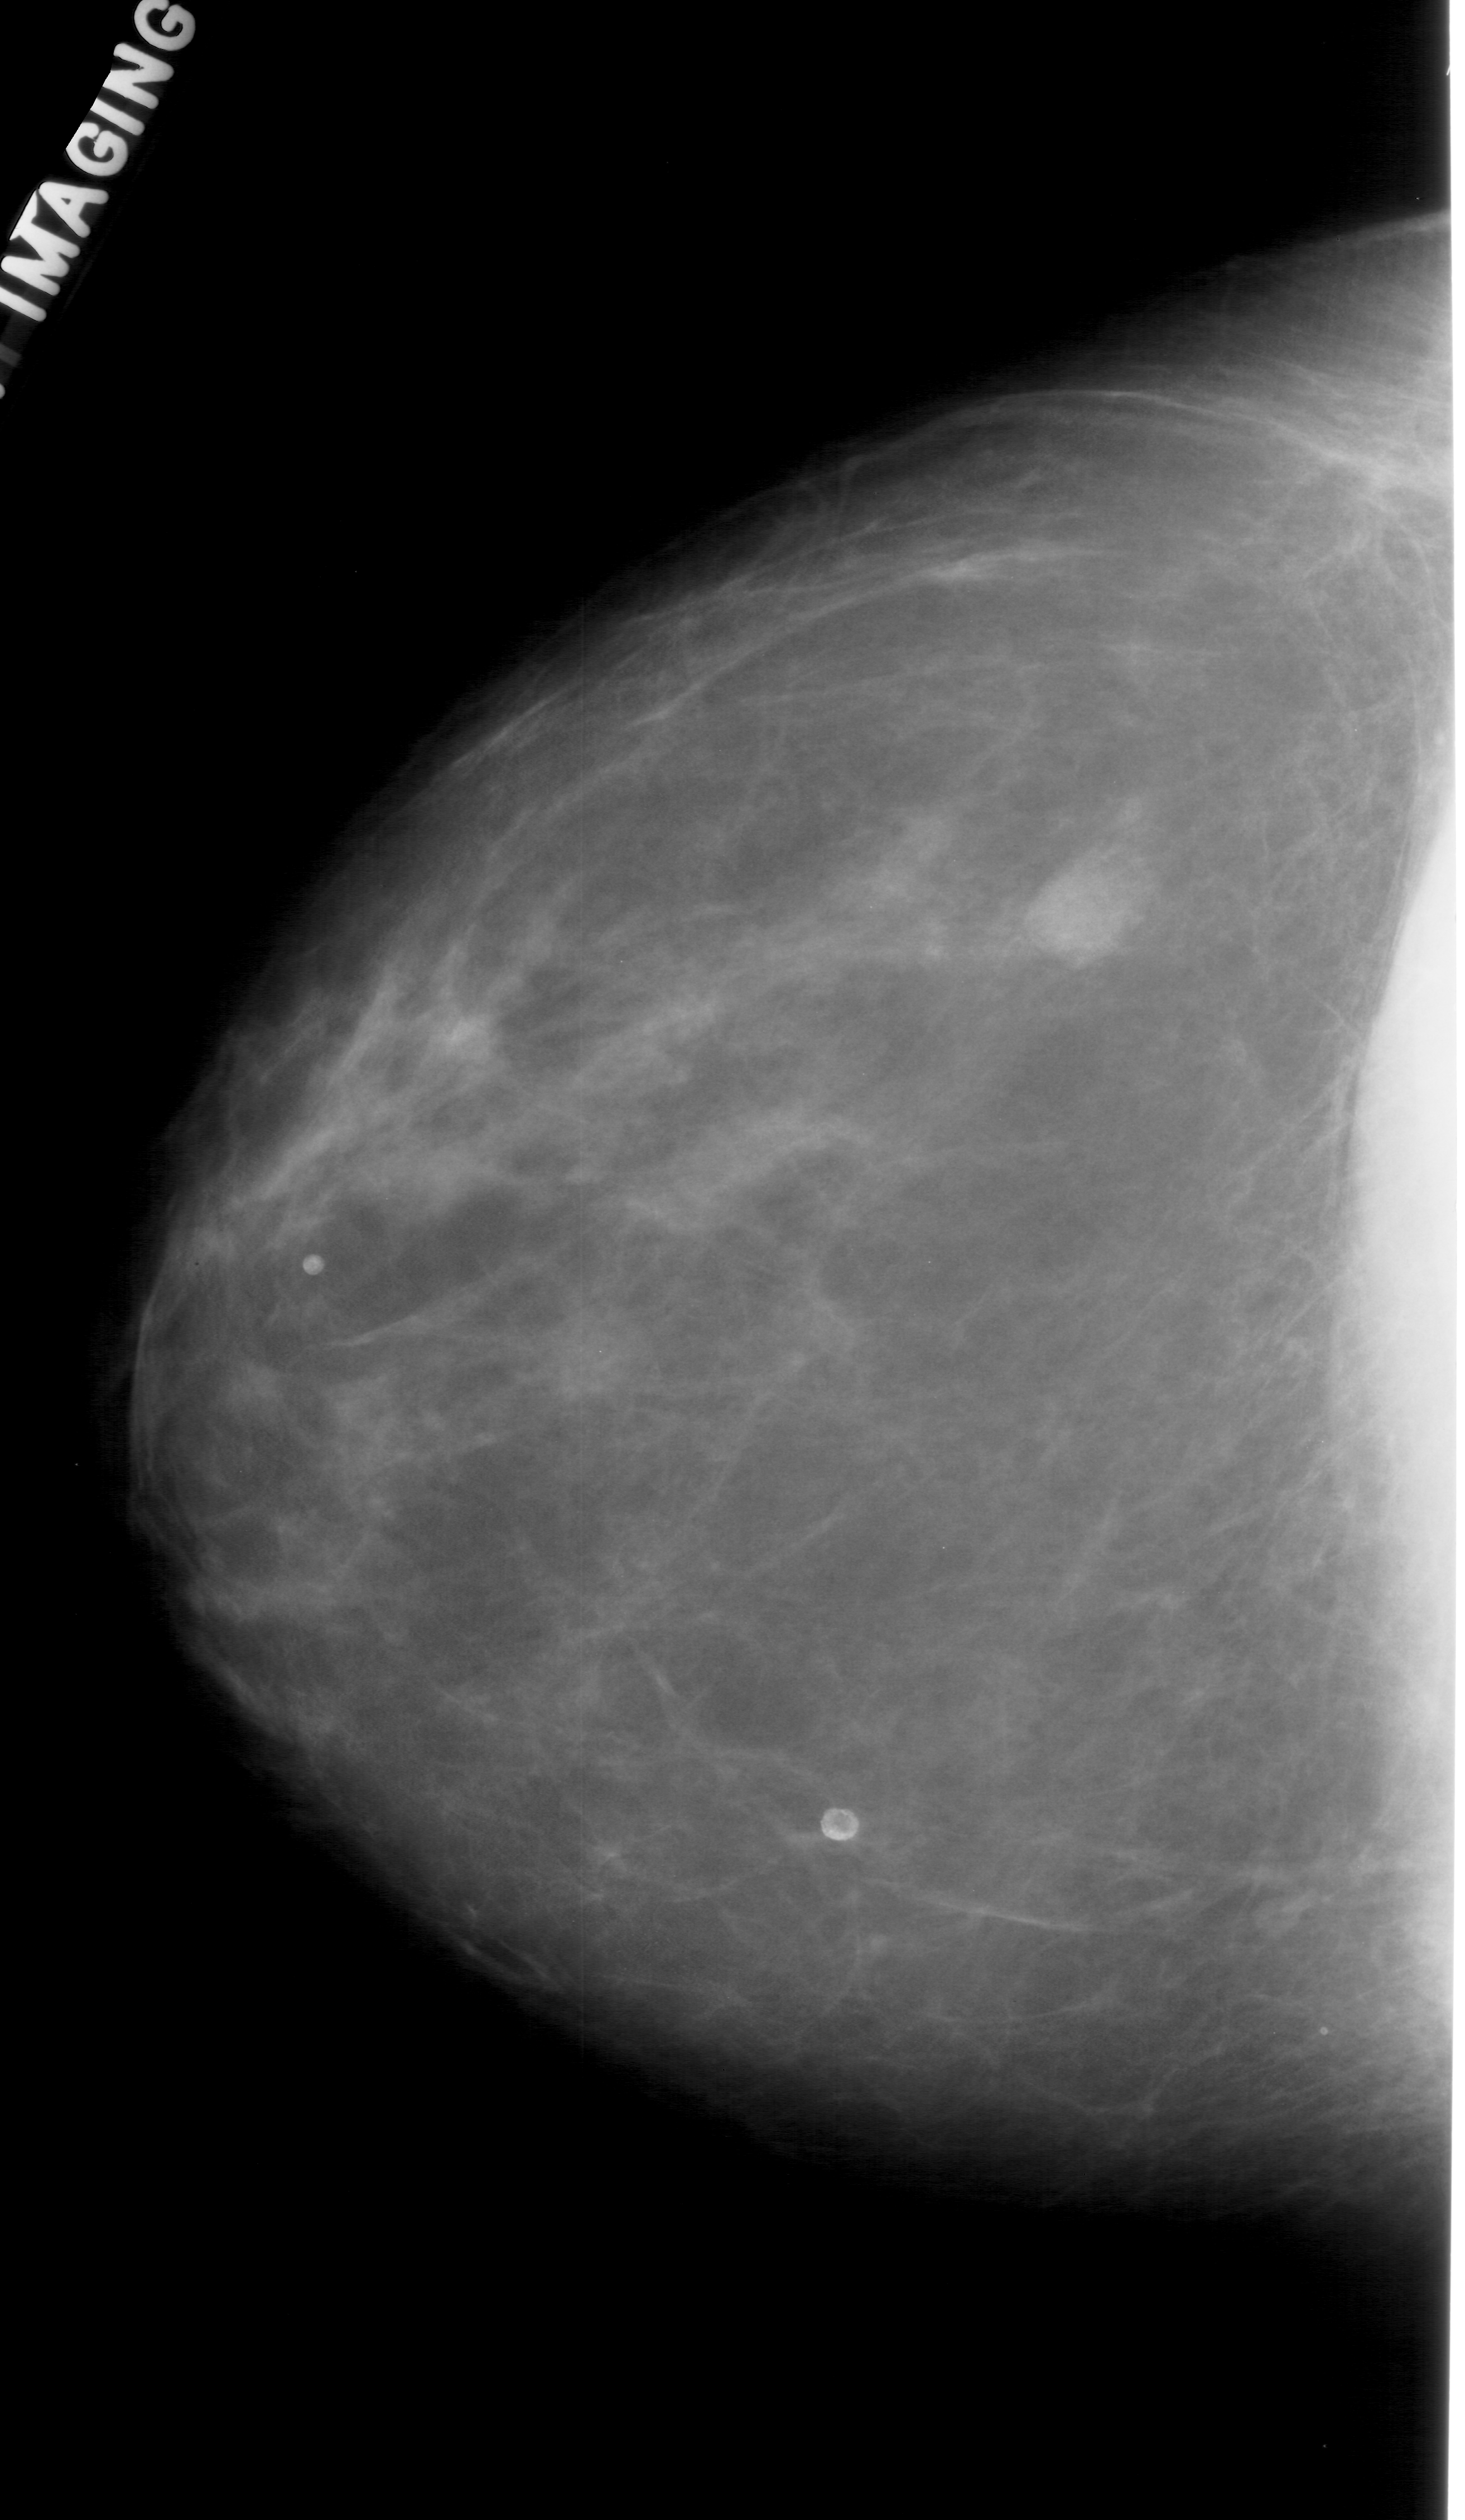
Mammogram (digitized film). Left breast. Craniocaudal (CC) view. Breast composition: scattered fibroglandular densities (BI-RADS density category 2 of 4). 1465 × 2520 image matrix.
Expert-marked regions of interest on this image (one box per marked abnormality):
- mass, shape lobulated, margins obscured; BI-RADS assessment category 4; subtlety rating 5 on a 1 (subtle) to 5 (obvious) scale; pathology (as recorded): benign: bounding box (x1, y1, x2, y2) in pixels: (1017, 849, 1147, 973)